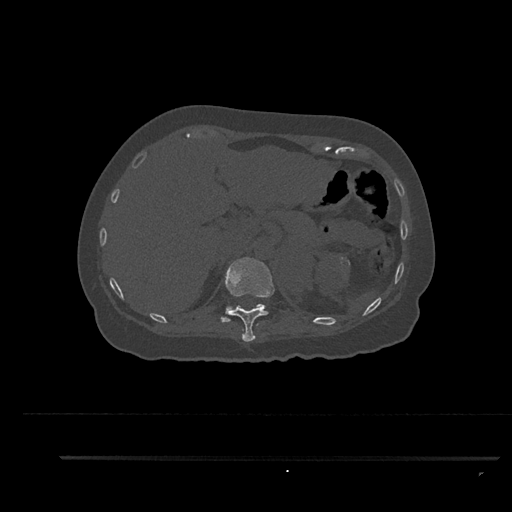
CT including the spine, one axial slice; position 303 of 797 along the scan axis; reconstruction kernel Br40s/3; 120 kVp; bone window (W 1800 / L 400 HU); 512 × 512 image matrix, field of view 408 × 408 mm. Patient: female, 44 years. From the clinical record (not read from this slice): primary cancer: renal; vertebrae with lytic lesions (as recorded): L1.
Structures marked on this image (semi-automatic segmentation, software-assisted and operator-edited):
- T11 vertebra: box from (x=225, y=257) to (x=275, y=342) px
- T12 vertebra: (x=220, y=304)–(x=266, y=323)